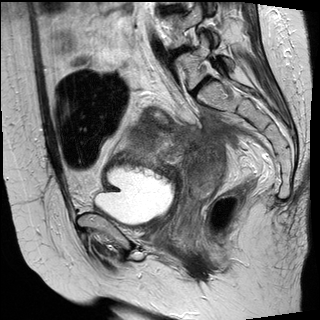
Pelvic MRI for cervical cancer, one sagittal slice; position 12 of 30 along the scan axis; T2-weighted; 1.5 T; TE 89 ms, TR 3810 ms; 320 × 320 image matrix, field of view 260 × 260 mm. Patient: female, 62 years.
Structures marked on this image (manually delineated by an expert):
- uterus and cervix: box from (x=128, y=125) to (x=225, y=200) px